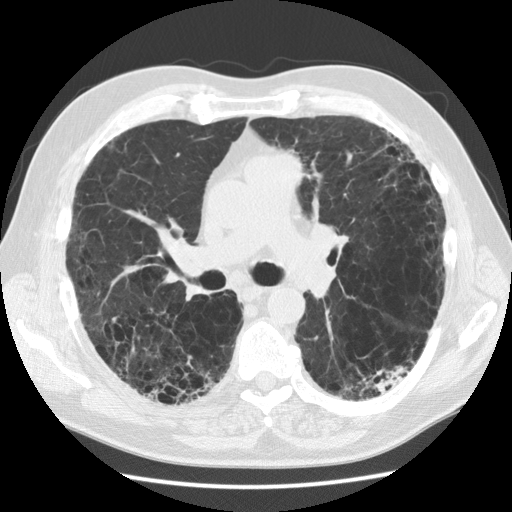
Low-dose screening chest CT, one axial slice. Lung window (W 1500 / L -600 HU). 2.5 mm slice thickness. 512 × 512 image matrix, field of view 360 × 360 mm.
Structures marked on this image (manually delineated by an expert):
- lesion 1 (tumor, lower lobe of left lung): box from (x=372, y=366) to (x=409, y=394) px